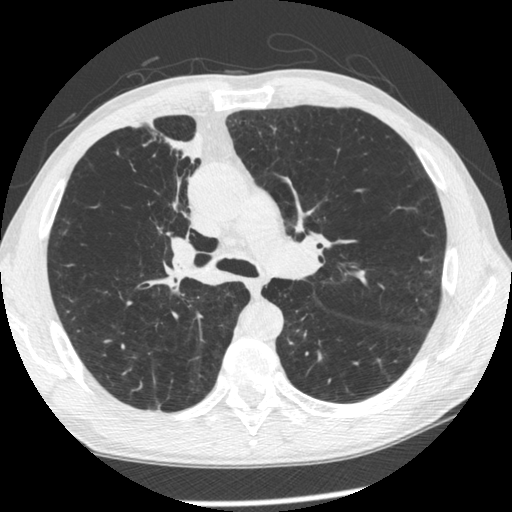
Low-dose screening chest CT, one axial slice; reconstruction kernel STANDARD; 120 kVp; lung window (W 1500 / L -600 HU); 1.25 mm slice thickness; 512 × 512 image matrix.
Annotated regions visible in this slice (expert manual segmentation):
- lesion 1 (tumor, upper lobe of right lung): bounding box <166,133,204,161> (left, top, right, bottom; pixels)